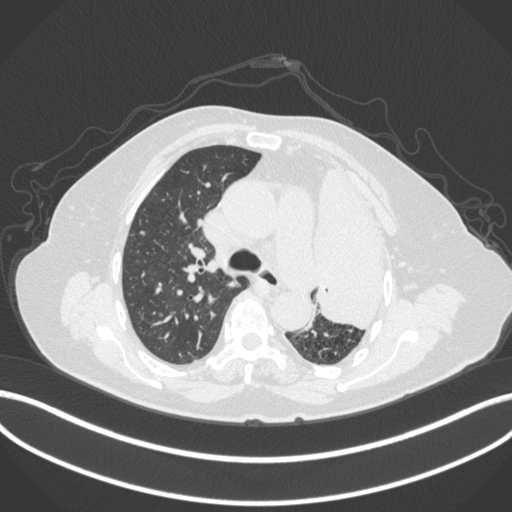
Chest CT, one axial slice. Slice 262 of 399 in the series (ordered by position). Reconstruction kernel B31f. 120 kVp. Lung window (W 1500 / L -600 HU). 512 × 512 image matrix, field of view 400 × 400 mm. Female patient, age 75 years. Case-level facts recorded for this patient, not image findings: clinical TNM (as recorded): T3 N3 M1.
Annotated regions visible in this slice (bounding box drawn by a radiologist):
- lung tumour (recorded histology: adenocarcinoma): bounding box <308,156,401,332> (left, top, right, bottom; pixels)